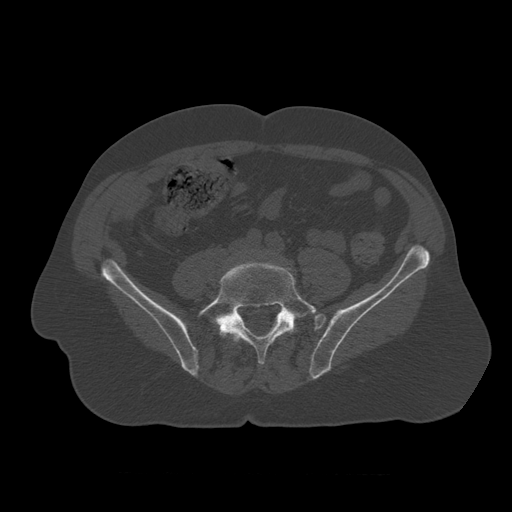
CT including the spine, one axial slice; slice 257 of 450 in the series (ordered by position); reconstruction kernel STANDARD; 120 kVp; bone window (W 1800 / L 400 HU); 512 × 512 image matrix, field of view 405 × 405 mm. Patient age 75 years. Case-level facts recorded for this patient, not image findings: primary cancer: prostate.
Outlined on this slice (semi-automatically segmented with operator editing):
- L4 vertebra: box from (x=229, y=271) to (x=235, y=334) px
- L5 vertebra: (x=198, y=261)–(x=317, y=365)